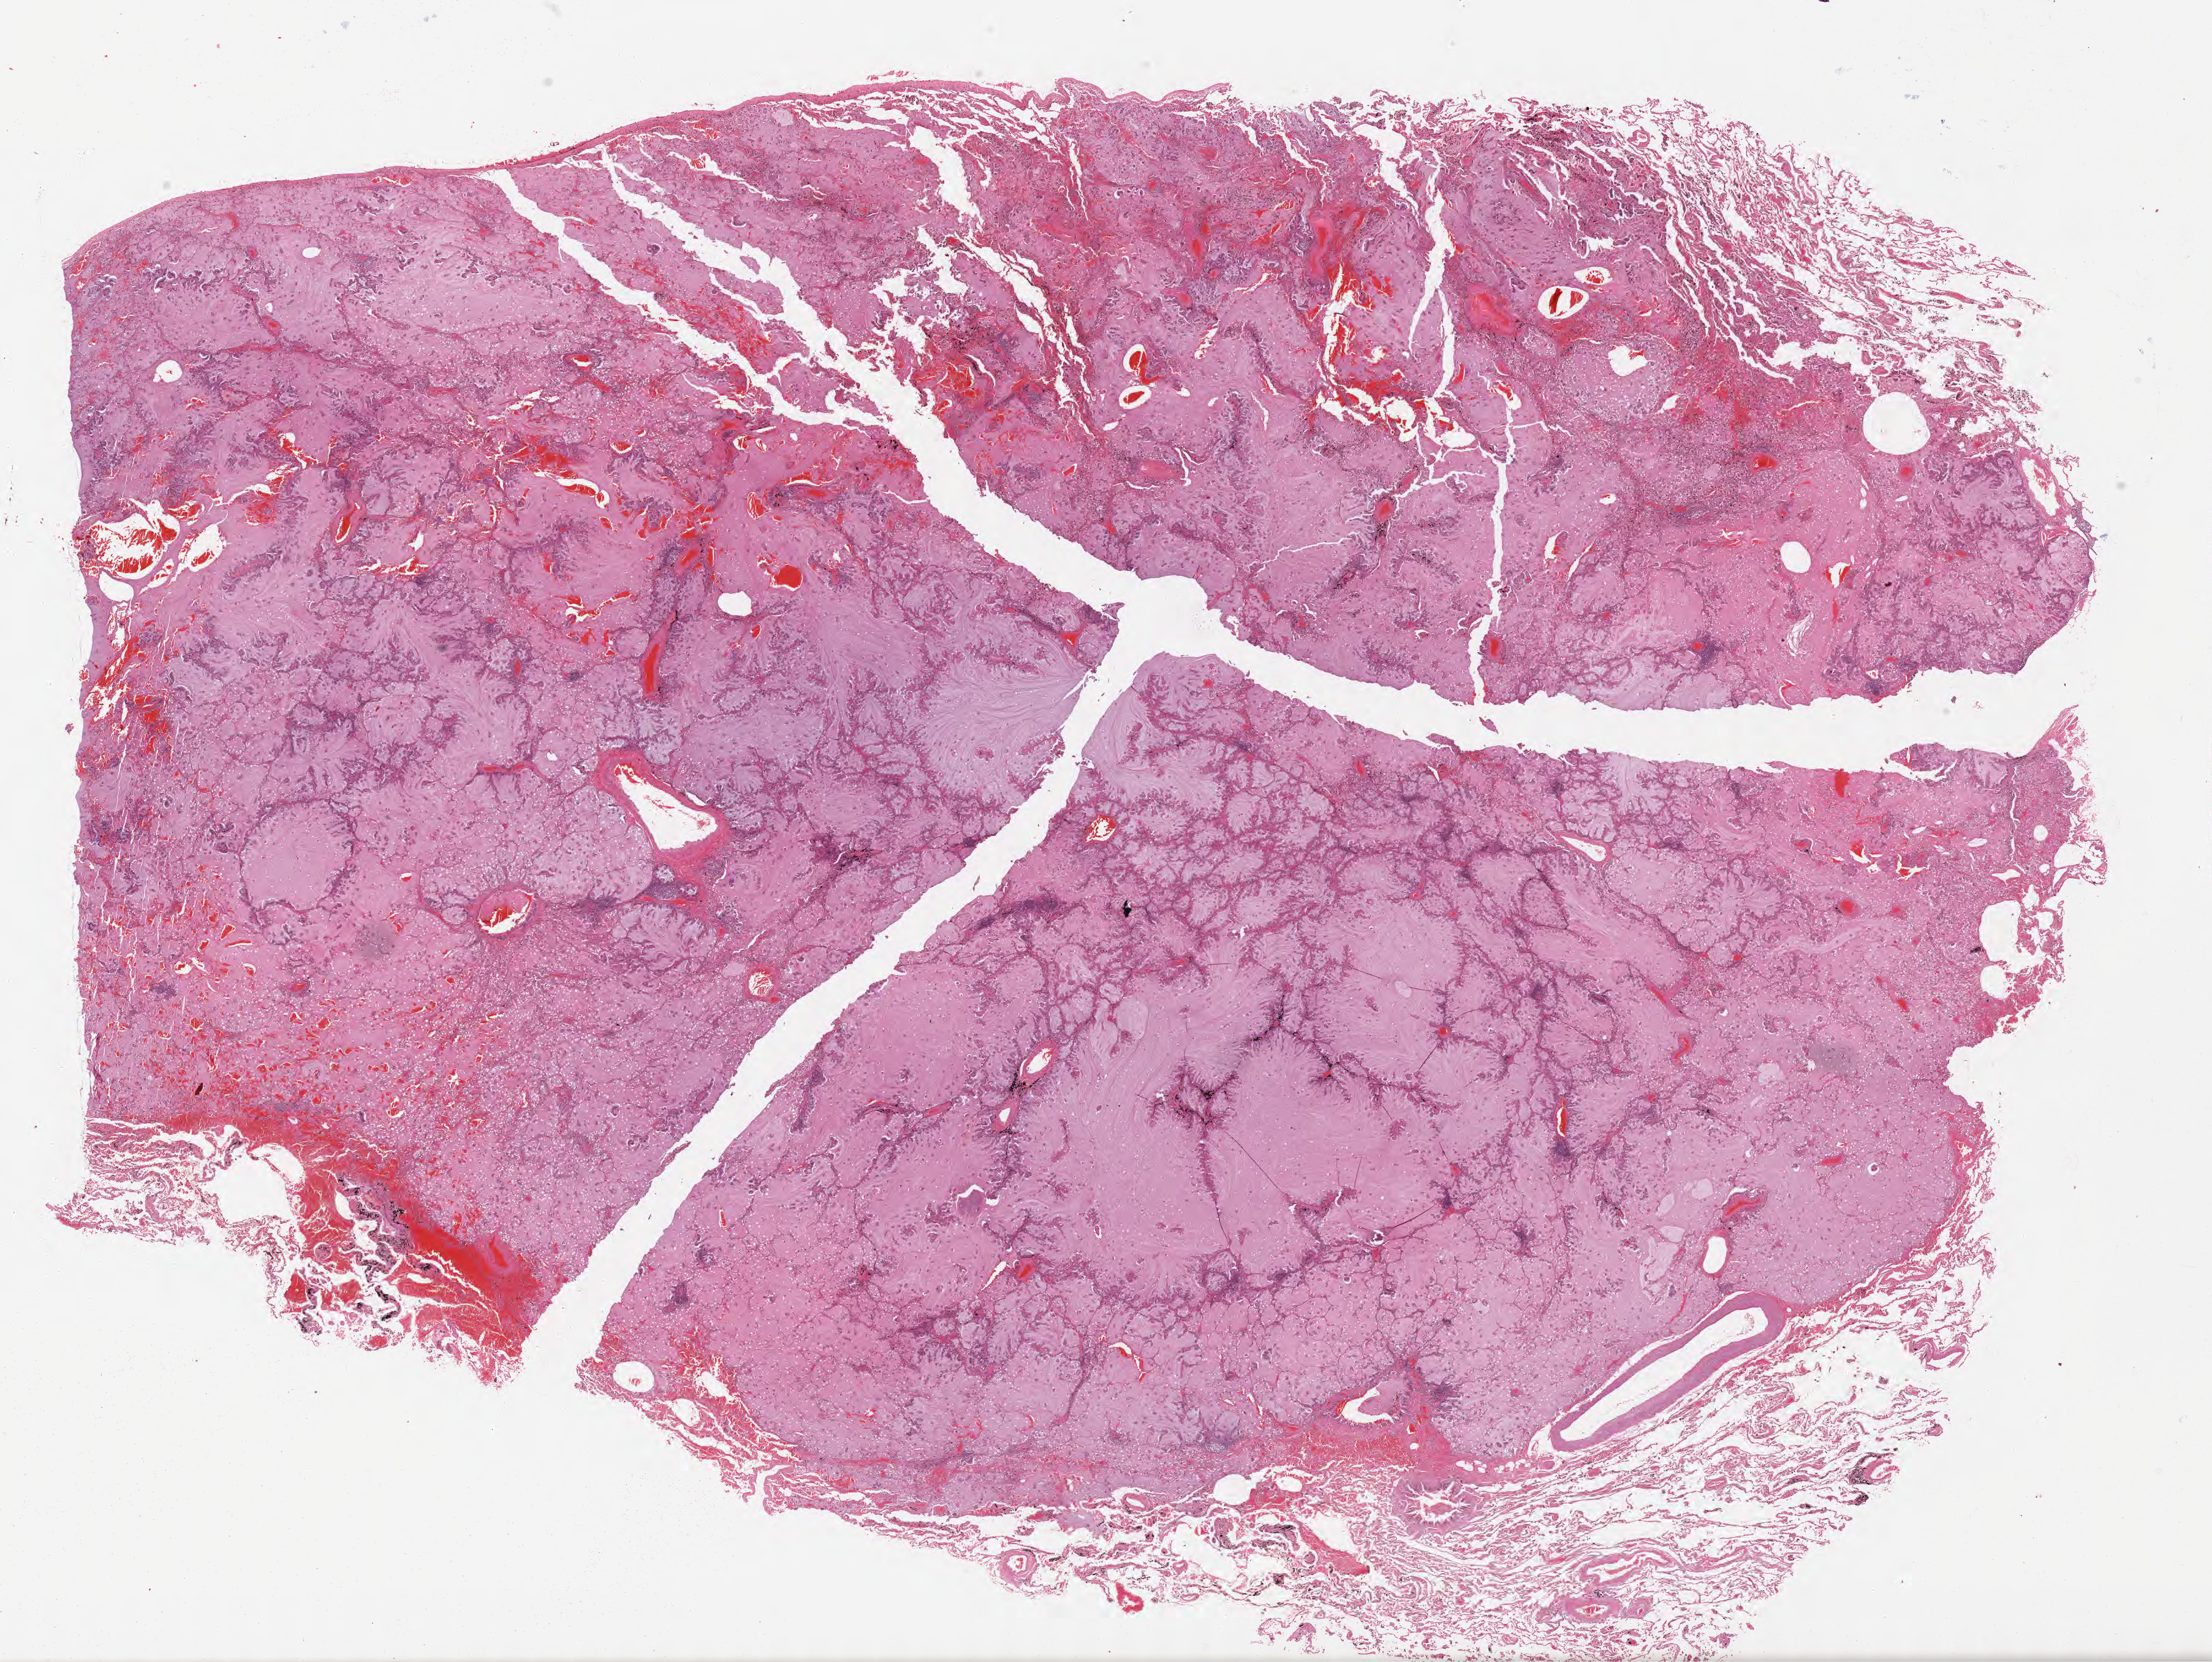
Whole-slide image, H&E stain, shown as a low-resolution overview of the whole scanned area (about 29.2 x 21.9 mm), formalin-fixed, paraffin-embedded (FFPE) tissue, specimen: primary tumor, anatomic site: upper lobe of right lung. Patient: male, 67 years old.
Diagnosis: Adenocarcinoma with mixed subtypes.